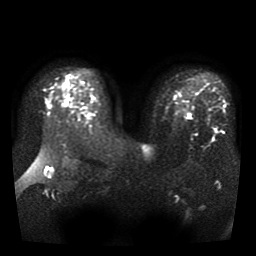
Breast MRI, one axial slice. Diffusion-weighted series; image 2 of 4 stored at this slice position (different b-values; order by instance number). 1.5 T. 5 mm slice thickness. 256 × 256 image matrix, field of view 330 × 330 mm. Female patient.
Annotated regions visible in this slice (outlined manually by an expert reader):
- tumour on diffusion-weighted imaging: bounding box (x1, y1, x2, y2) in pixels: (187, 113, 191, 119)